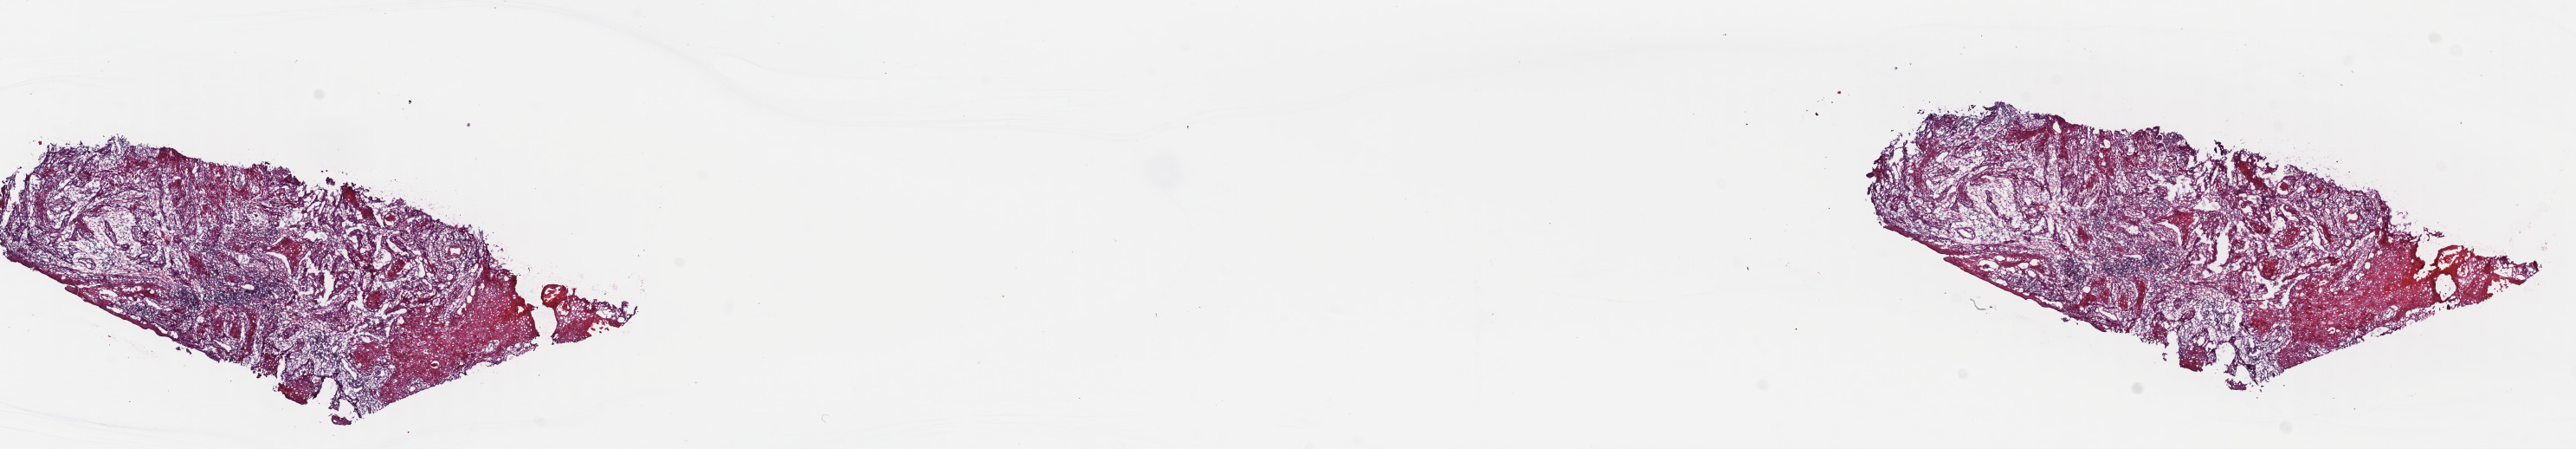
Digitized H&E-stained tissue section (whole slide) — a low-resolution overview of the entire scanned area, about 23.4 x 4.1 mm (acquisition: 40x scan); frozen section from the top of the tissue portion; sample: primary tumour, head and neck. Female, age 67 years at initial diagnosis. Histologic grade: G2 (moderately differentiated). Composition of this section per pathologist review: tumour cells 65%, tumour nuclei 90%, normal cells 0%, stromal cells 35%, necrosis 0%. Inflammatory infiltration, as recorded: lymphocyte infiltration 10%, monocyte infiltration 2%, neutrophil infiltration 1%.
AJCC pathologic stage: III (7th edition). Pathologic diagnosis: Squamous cell carcinoma, keratinizing, NOS. Lymph nodes positive (case pathology): 0 of 10 examined. Laterality: right. TNM: T3 N0 M0.